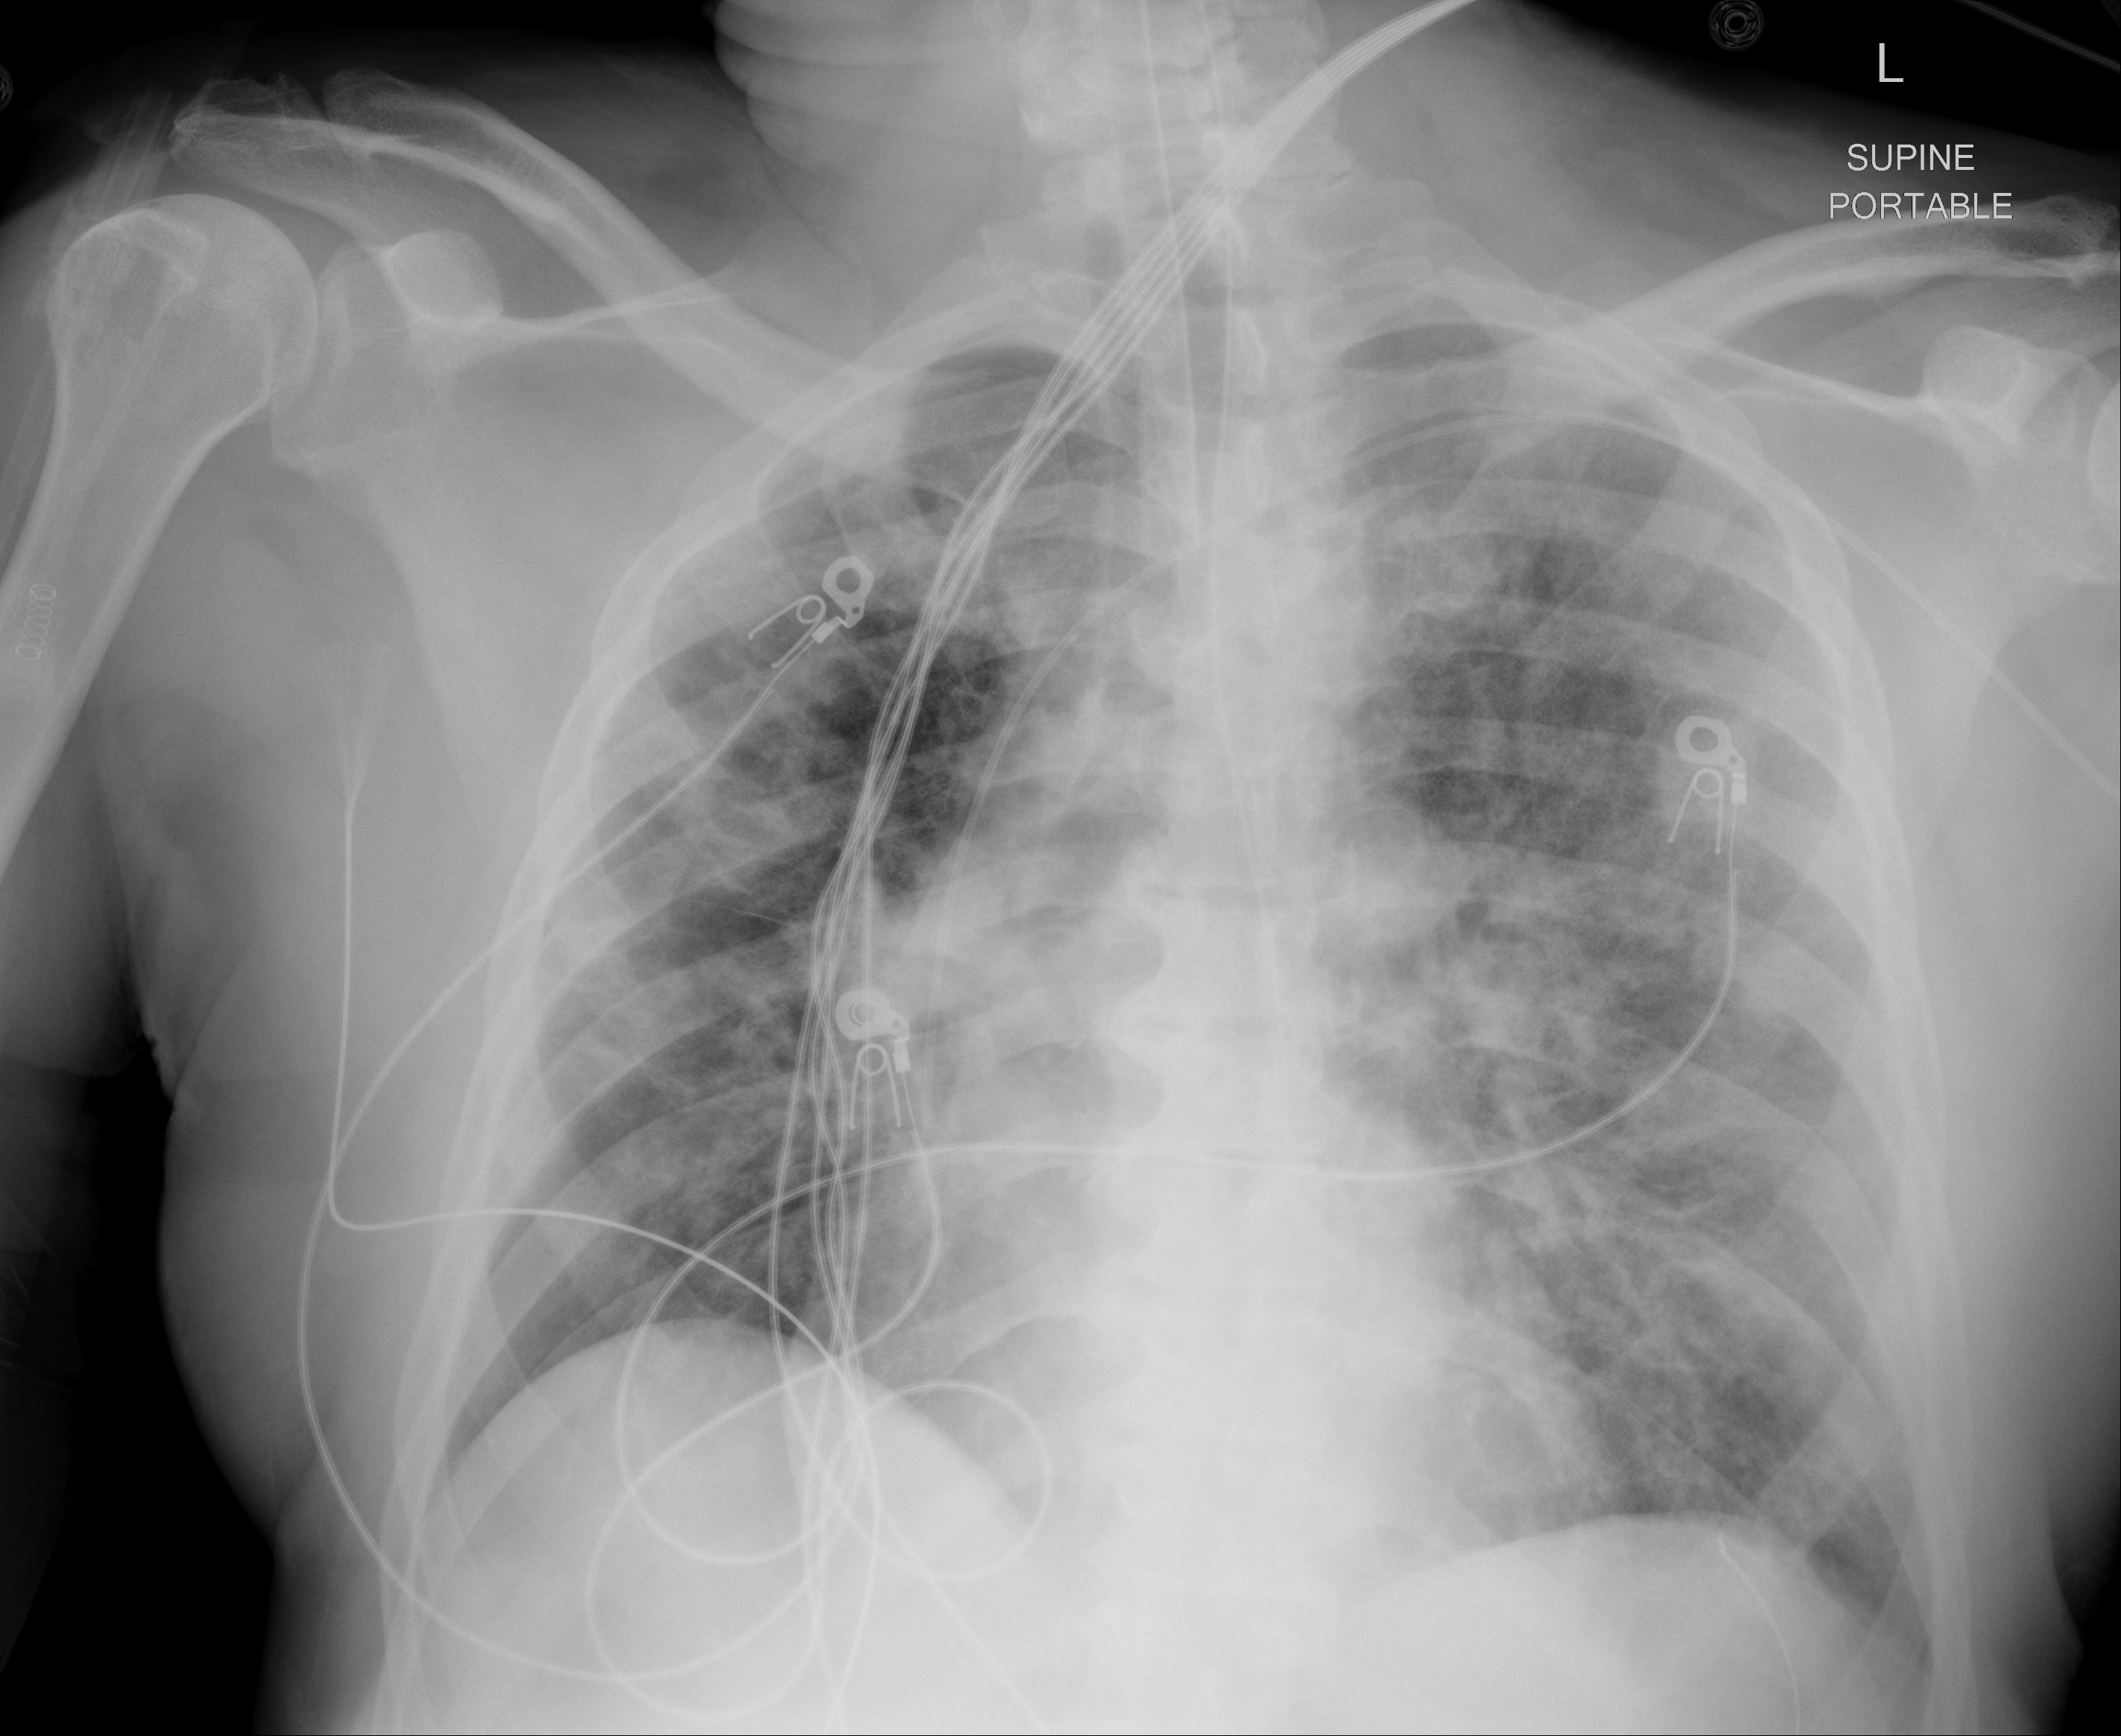
Chest X-ray (portable), AP projection. Male patient, age 64 years; imaged 0 days after the COVID-19 diagnosis.
Radiologist key findings (as recorded): increased patchy opacities throughout the lungs bilaterally.